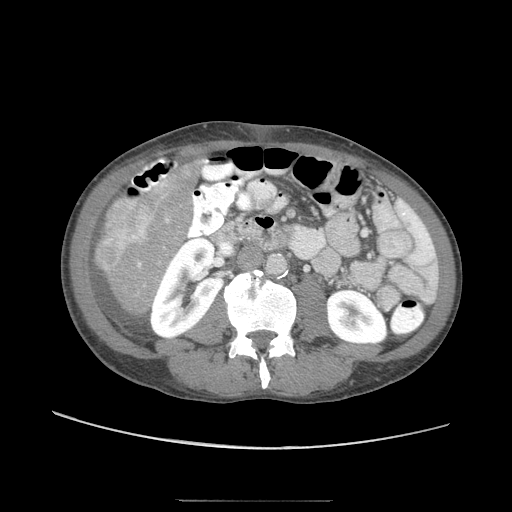
Contrast-enhanced abdominal CT (liver protocol), one axial slice. Slice 13 of 103 in the series (ordered by position). 120 kVp. Soft-tissue window (W 400 / L 40 HU). 512 × 512 image matrix, field of view 380 × 380 mm. From the clinical record (not read from this slice): diagnosis: hepatocellular carcinoma (patient treated with transarterial chemoembolisation; whether this scan precedes or follows treatment is not stated here); TNM stage (as recorded): Stage-IIIA; Child-Pugh class: A; tumour size: 16 cm.
Structures marked on this image (semi-automatic segmentation, software-assisted and operator-edited):
- liver parenchyma outside the tumour (the mass and vessels are separate outlines, so this box may not span the whole liver): bounding box [x1, y1, x2, y2] px = [92, 158, 204, 317]
- mass: [93, 189, 152, 273]
- liver vessels: [149, 202, 159, 223]